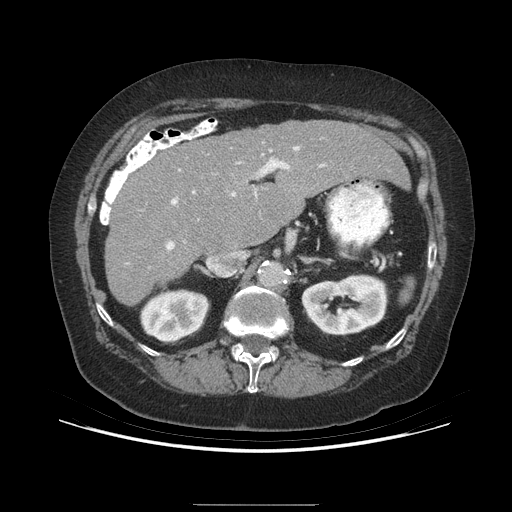
Contrast-enhanced abdominal CT (liver protocol), one axial slice. Slice 154 of 192 in the series (ordered by position). Reconstruction kernel STANDARD. 140 kVp. Soft-tissue window (W 400 / L 40 HU). 512 × 512 image matrix, field of view 400 × 400 mm. From the clinical record (not read from this slice): diagnosis: hepatocellular carcinoma (patient treated with transarterial chemoembolisation; whether this scan precedes or follows treatment is not stated here); TNM stage (as recorded): Stage-I; Child-Pugh class: A; tumour differentiation: moderately differentiated; tumour size: 3.2 cm.
Annotated regions visible in this slice (semi-automatic segmentation, software-assisted and operator-edited):
- liver parenchyma outside the tumour (the mass and vessels are separate outlines, so this box may not span the whole liver): box from (x=104, y=120) to (x=408, y=304) px
- liver vessels: (x=166, y=146)–(x=324, y=250)